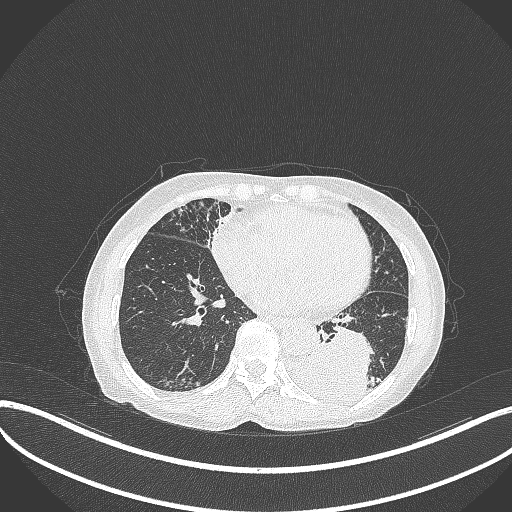
Chest CT, one axial slice. Slice 108 of 370 in the series (ordered by position). Lung window (W 1500 / L -600 HU). 1 mm slice thickness. 512 × 512 image matrix, field of view 400 × 400 mm. Female patient, age 78 years. Case-level facts recorded for this patient, not image findings: clinical TNM (as recorded): T3 N0 M1.
Annotated regions visible in this slice (bounding box drawn by a radiologist):
- lung tumour (recorded histology: squamous cell carcinoma): bounding box (x1, y1, x2, y2) in pixels: (282, 327, 371, 411)